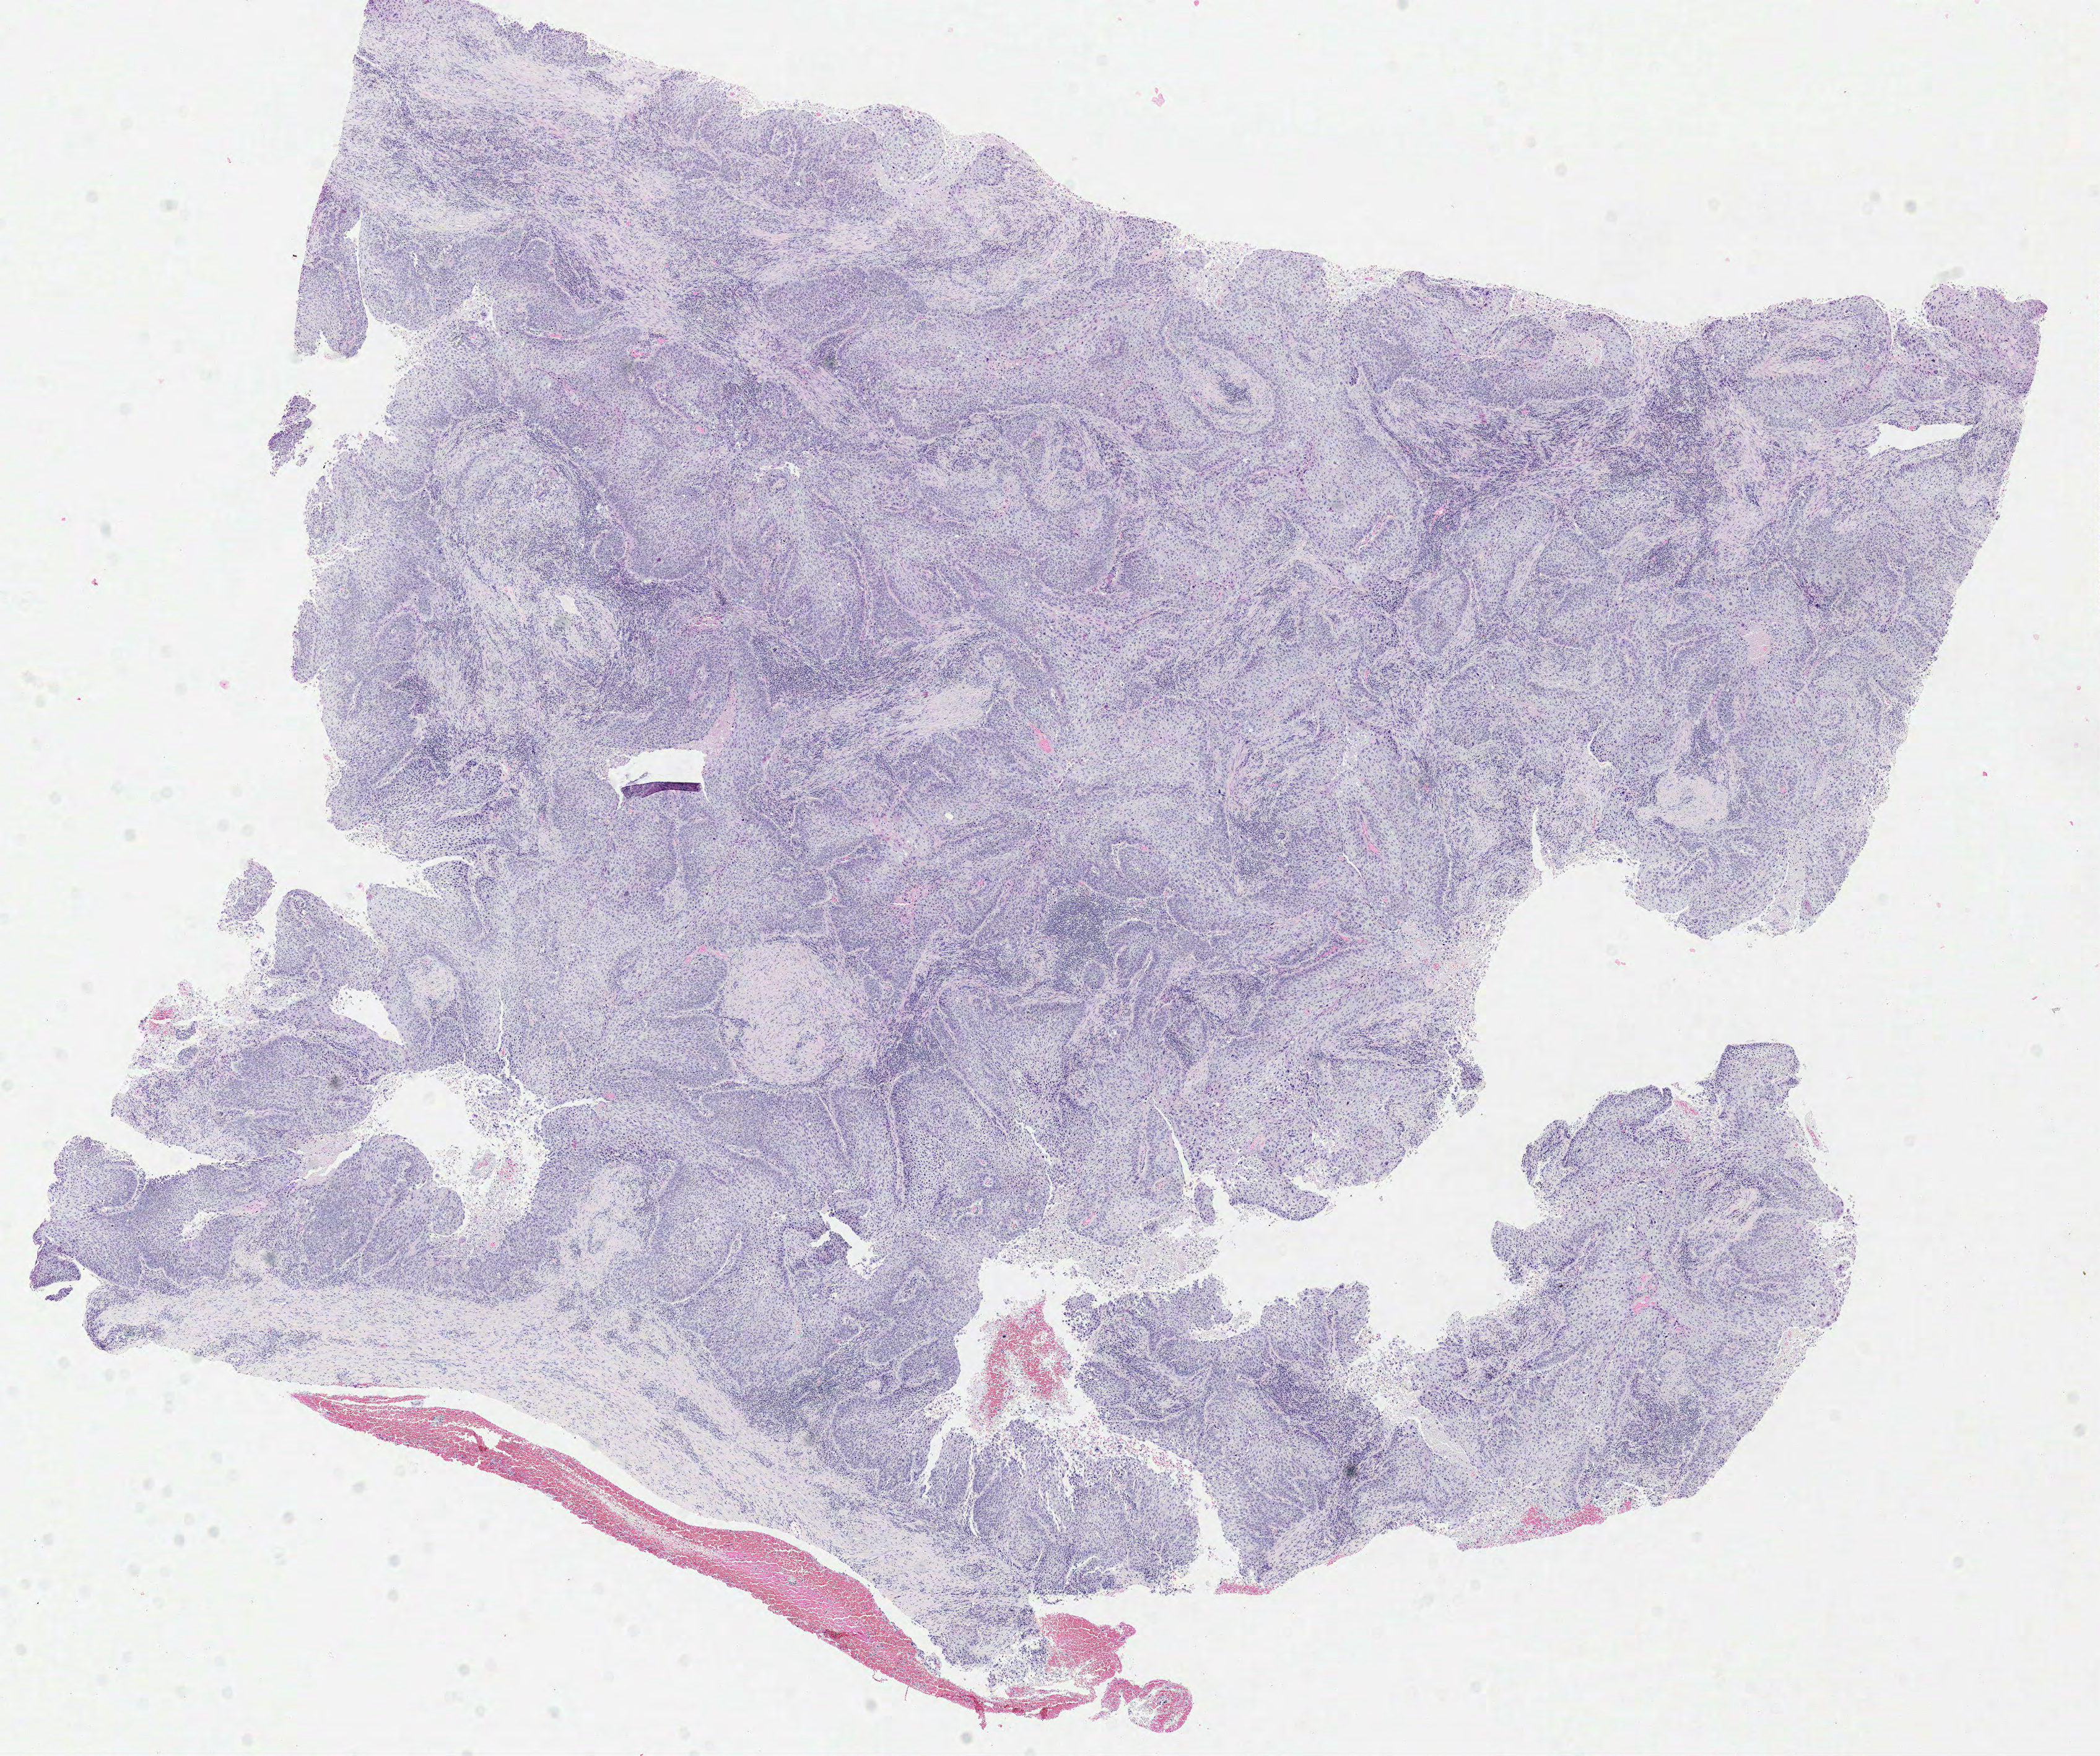
Digitized Hematoxylin and eosin (H&E) stained tissue section (whole slide) — shown as a low-resolution overview of the whole scanned area (about 13.4 x 11.2 mm); formalin-fixed paraffin-embedded (FFPE) diagnostic section; lung, primary tumour sample. Male patient; age at initial diagnosis 66 years.
Diagnosis: Squamous cell carcinoma, NOS (lower lobe, lung).